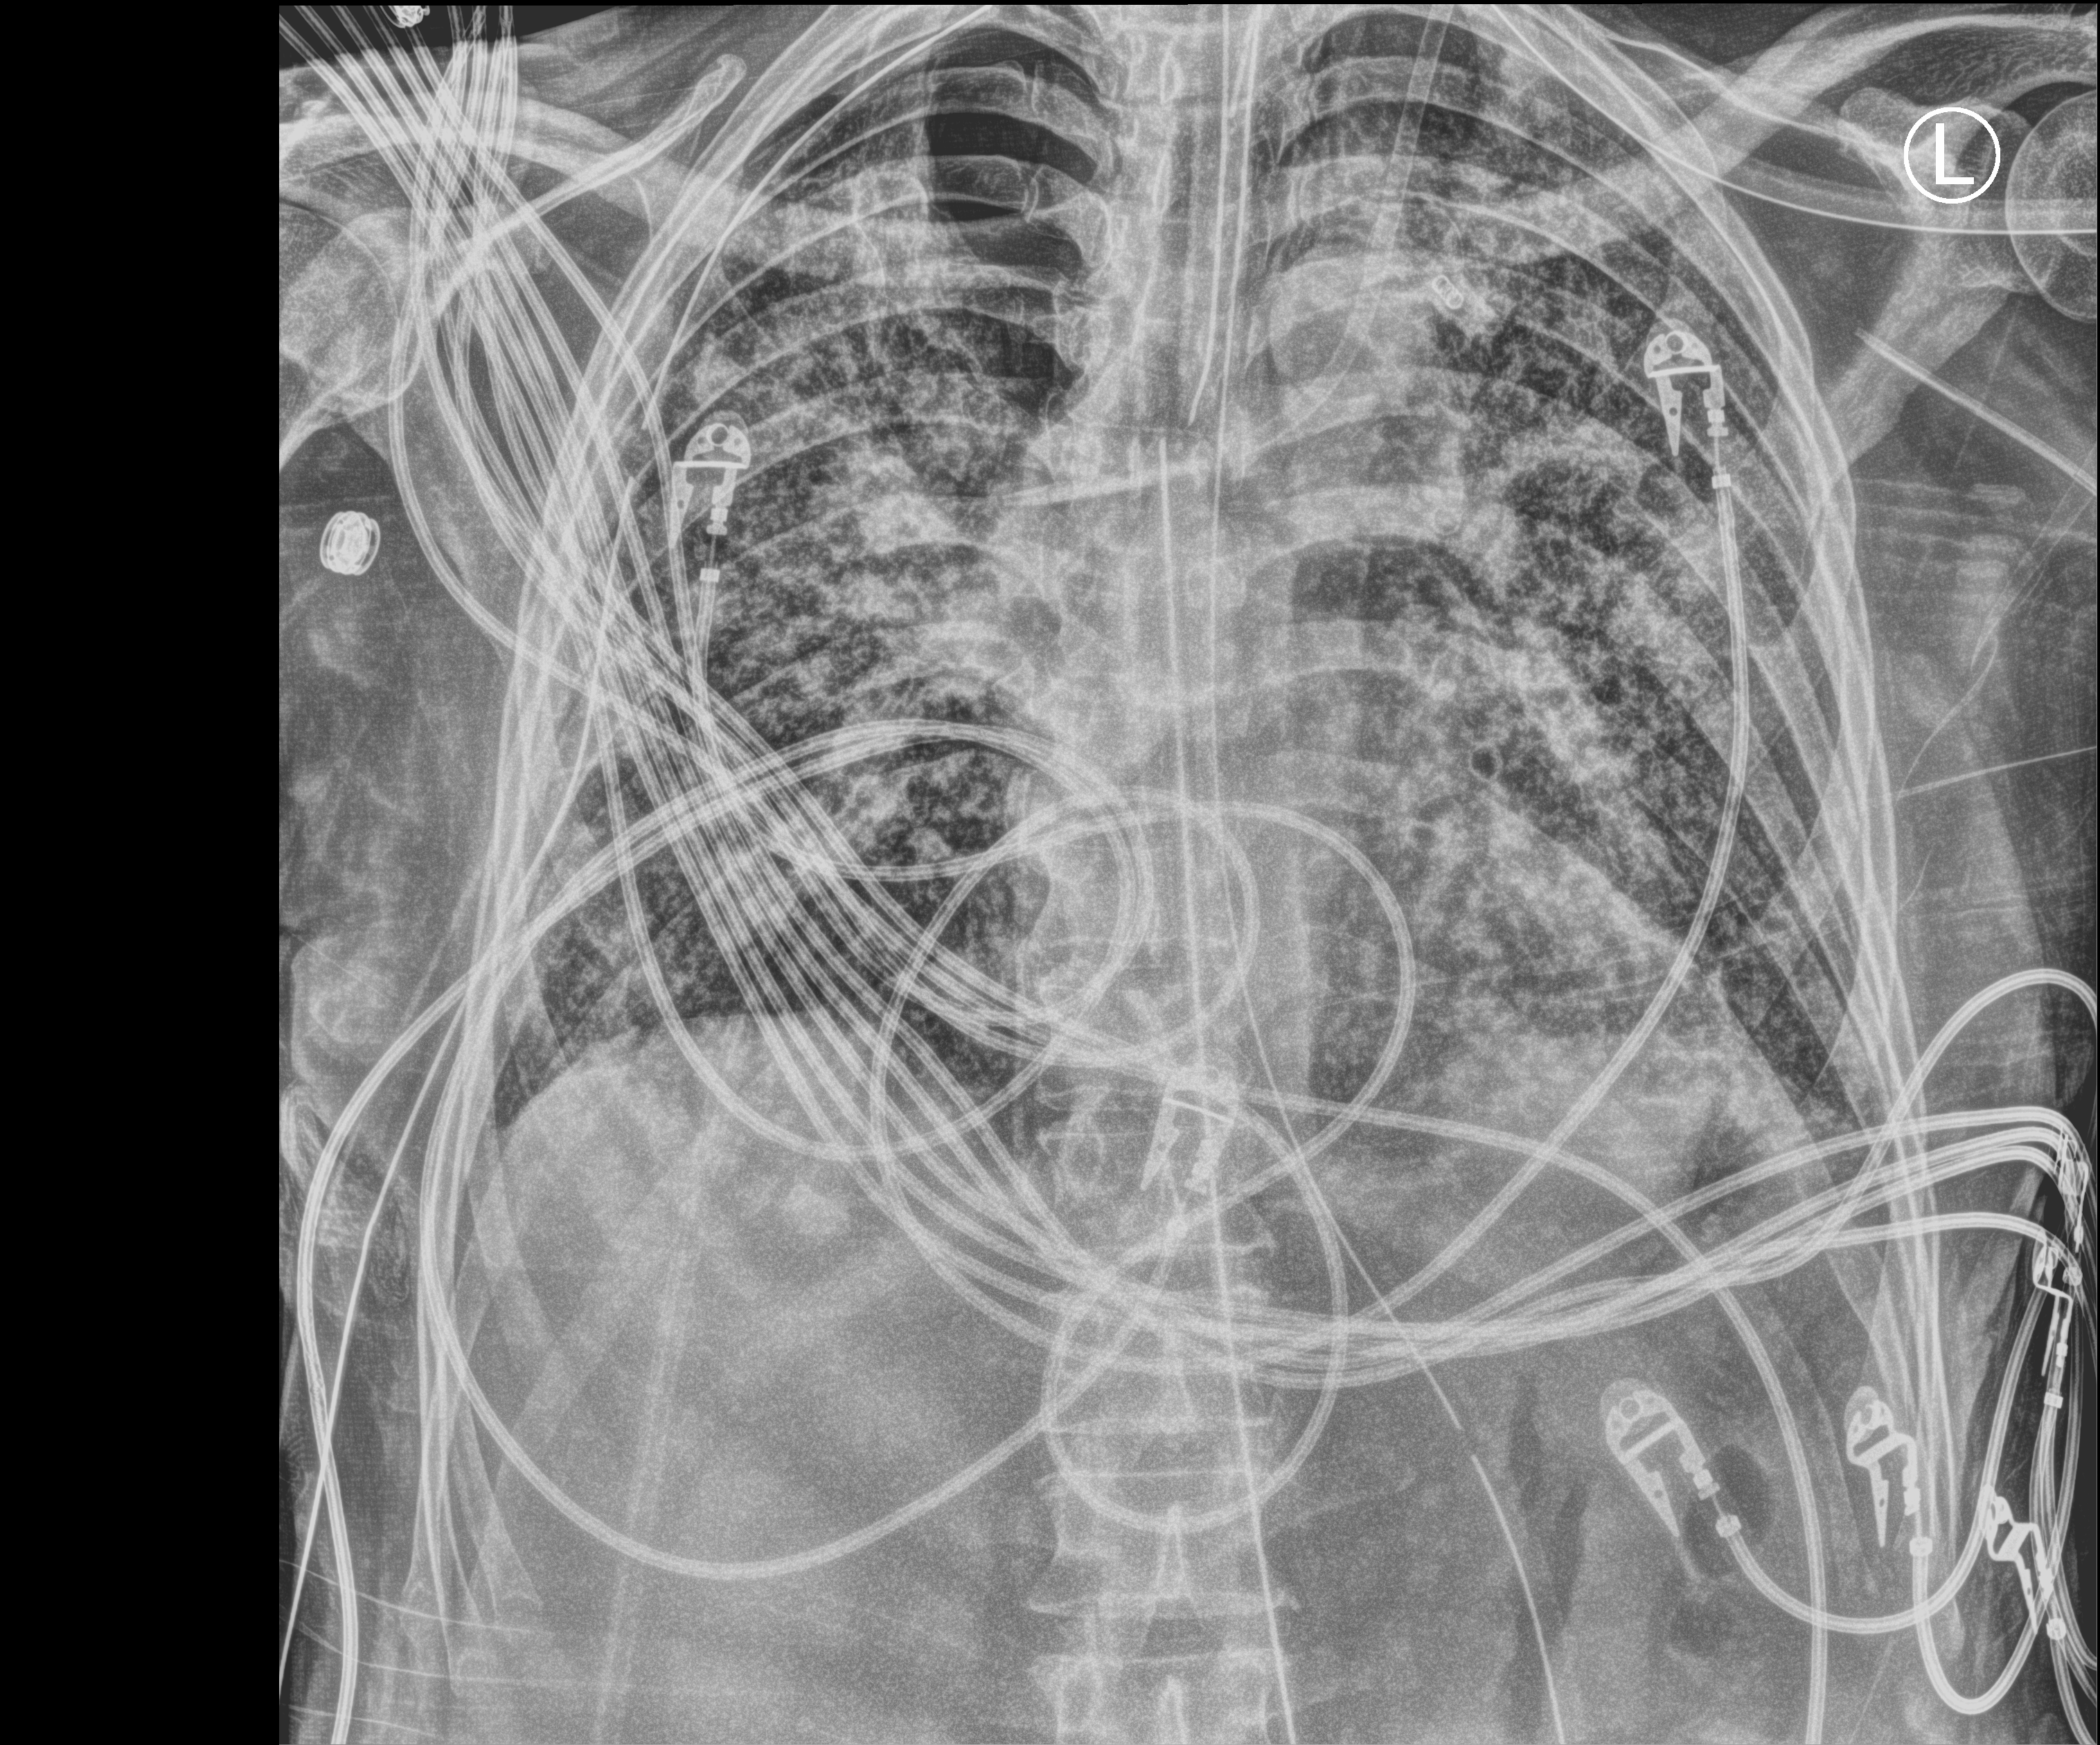
Chest X-ray (portable), anteroposterior (AP) projection. Male patient hospitalised with COVID-19, age 60–74 years.
Hospital-stay facts (about this admission, not read from this image; timing relative to this image not recorded): mechanically ventilated during this hospital stay: yes.